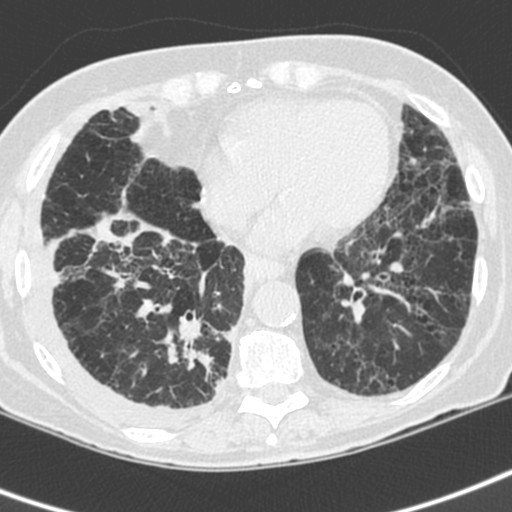
Low-dose screening chest CT, axial slice; baseline screening round; lung window (W 1500 / L -600 HU); standard (soft-tissue) reconstruction kernel (C); 120 kVp. Female, age 73 years at enrolment. Current smoker at enrolment.
- Lesion marked by an expert reader, bounding box <154,314,235,406> (left, top, right, bottom; pixels).
- Screening reader's record for this exam (one nodule recorded; not confirmed to be the boxed lesion): non-calcified nodule or mass ≥4 mm, right lower lobe, 35 × 30 mm, spiculated (stellate) margins, soft tissue attenuation.
- Official screen result: positive, change unspecified: nodule(s) >= 4 mm or enlarging nodule(s), mass(es), or other non-specific abnormalities suspicious for lung cancer.
- Lung cancer was diagnosed 22 days after this screen: adenocarcinoma, NOS, right lower lobe, stage IV (AJCC 6th edition), 35 mm at pathology.